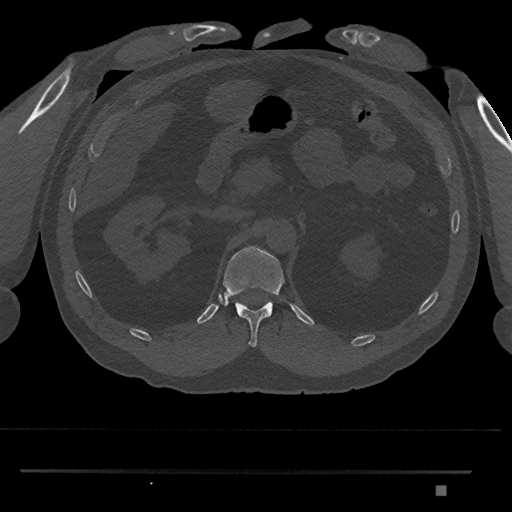
CT including the spine, one axial slice. Position 877 of 1134 along the scan axis. Reconstruction kernel Br40s/3. Bone window (W 1800 / L 400 HU). 512 × 512 image matrix, field of view 429 × 429 mm. Patient: male, 65 years. From the clinical record (not read from this slice): primary cancer: prostate.
Annotated regions visible in this slice (semi-automatic segmentation, software-assisted and operator-edited):
- T12 vertebra: bounding box [x1, y1, x2, y2] px = [221, 246, 285, 347]